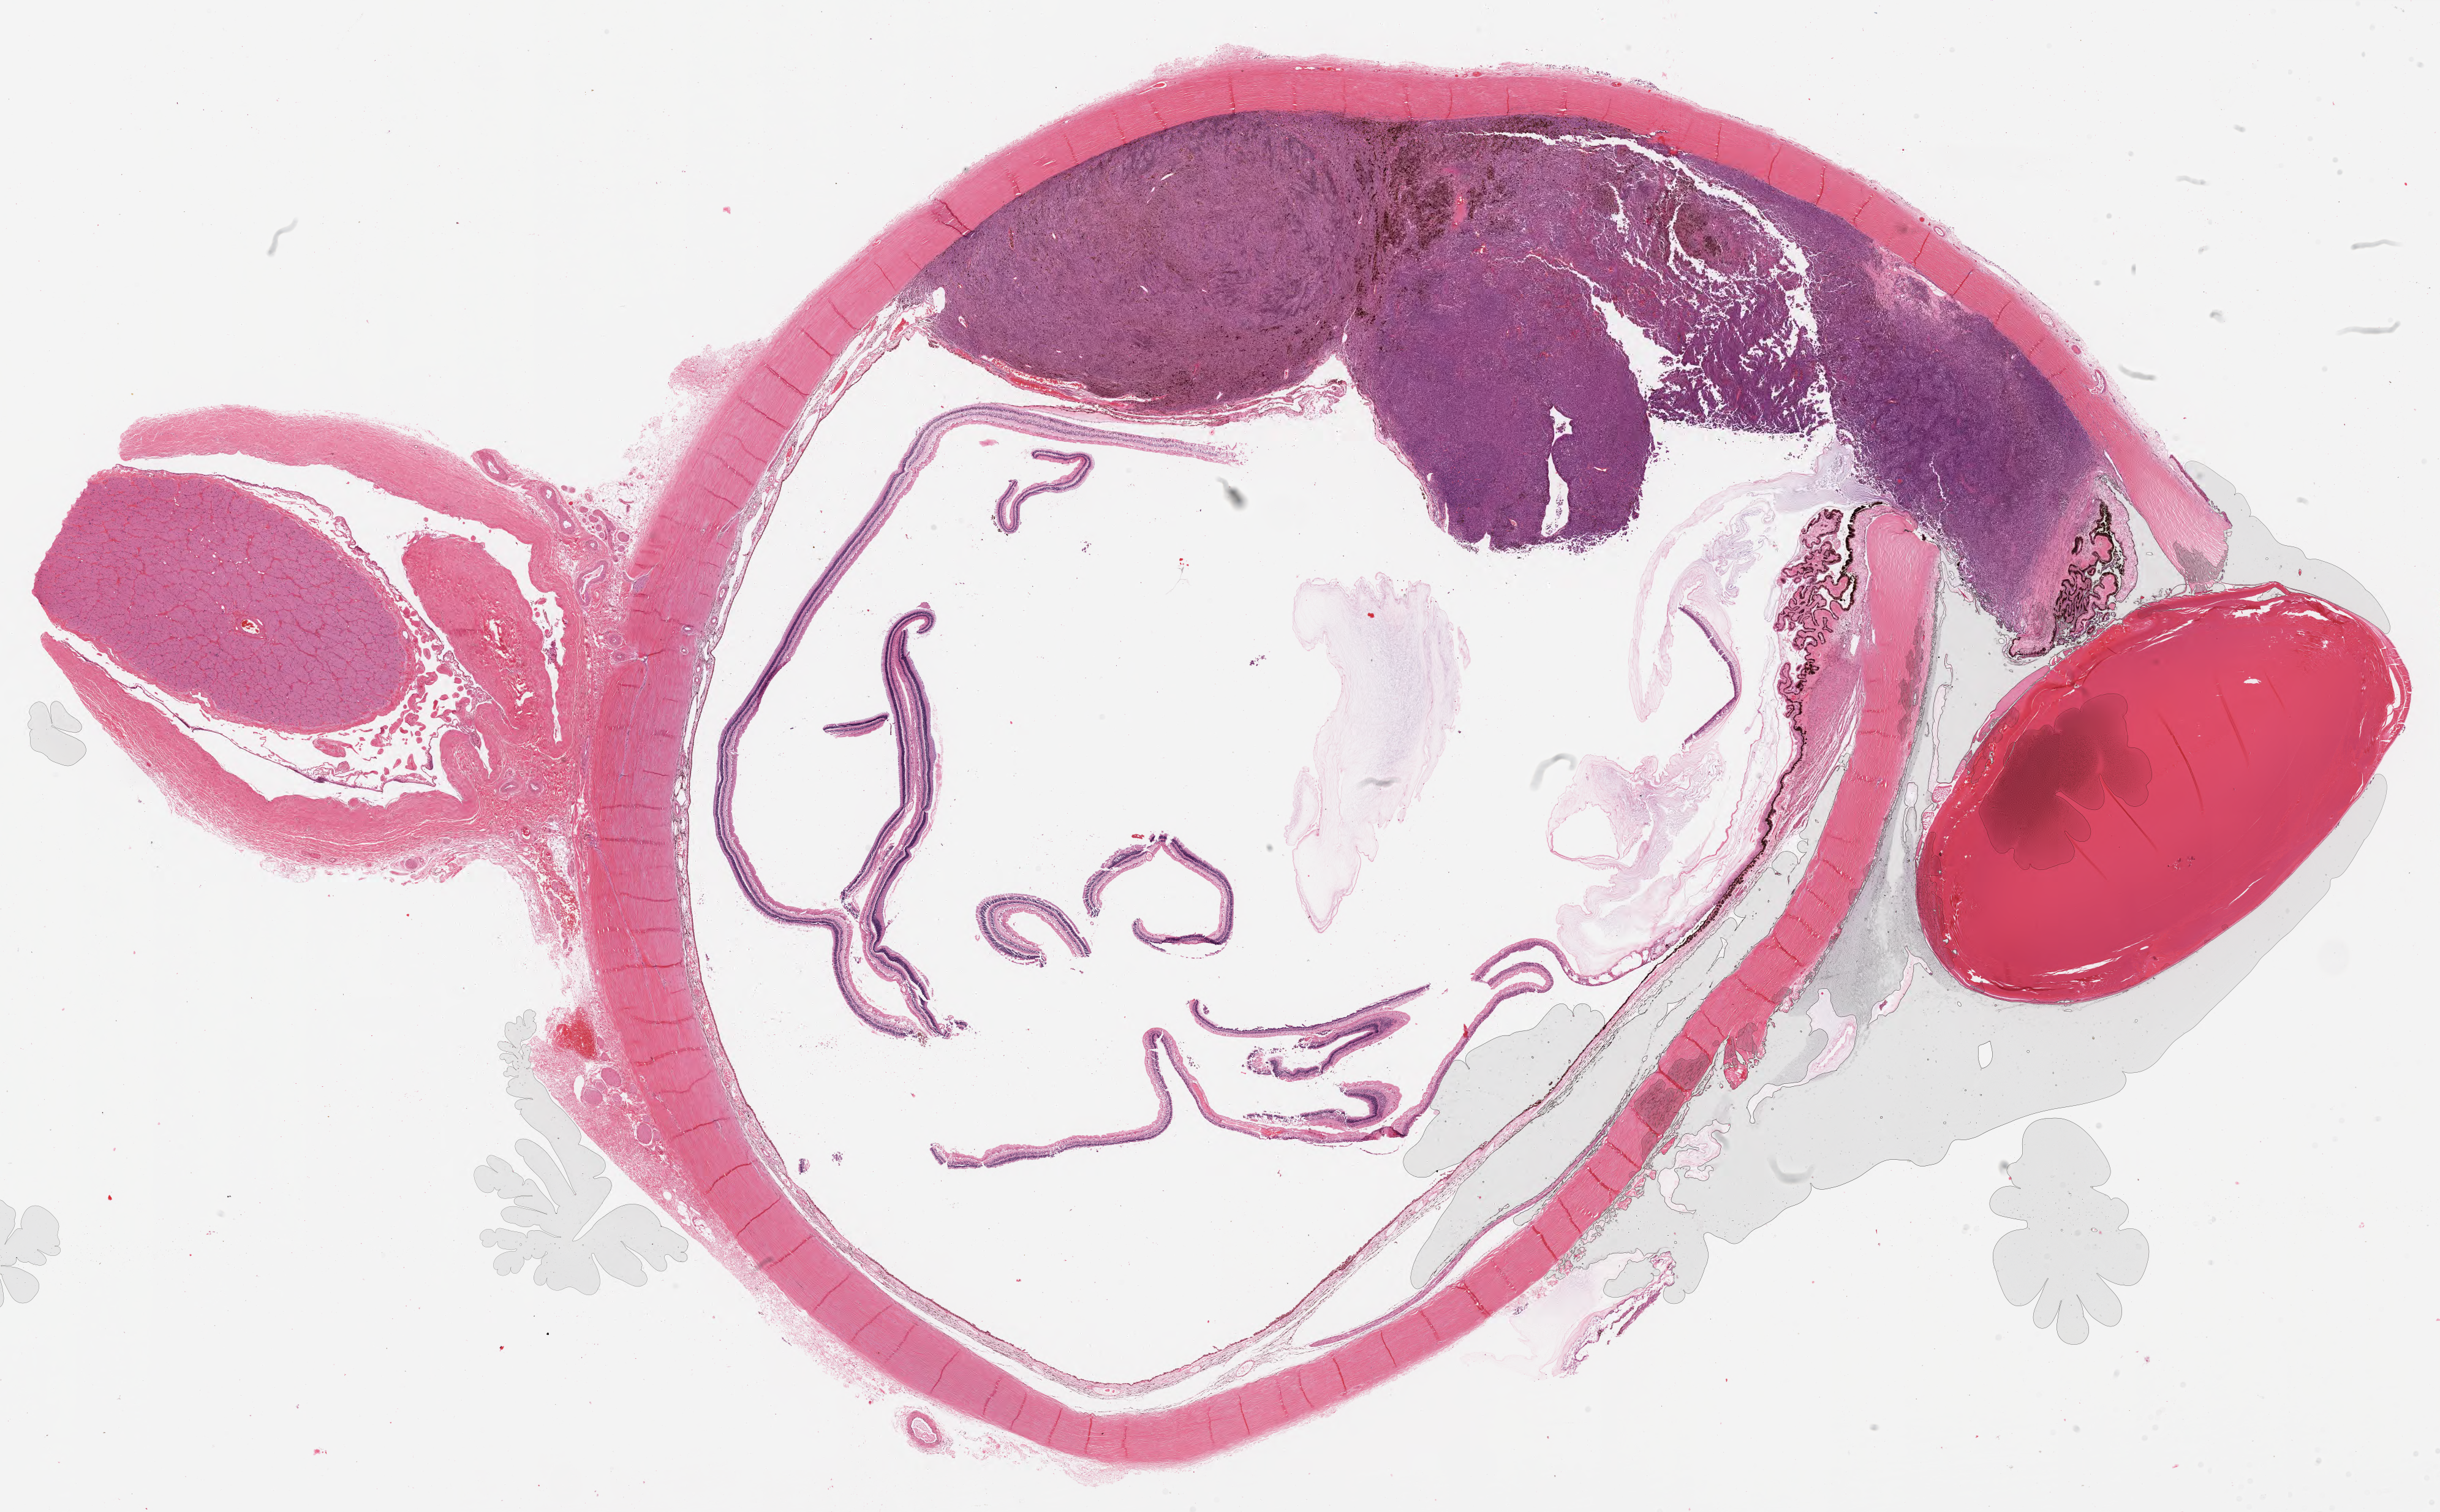
Whole-slide histology image, Hematoxylin and eosin (H&E) stained — whole scanned area (about 31.5 x 19.5 mm) shown as a low-resolution overview, formalin-fixed paraffin-embedded (FFPE) diagnostic section, primary tumour sample from the uvea. Patient: male, age at initial diagnosis 56 years.
Pathologic diagnosis: Mixed epithelioid and spindle cell melanoma (choroid).